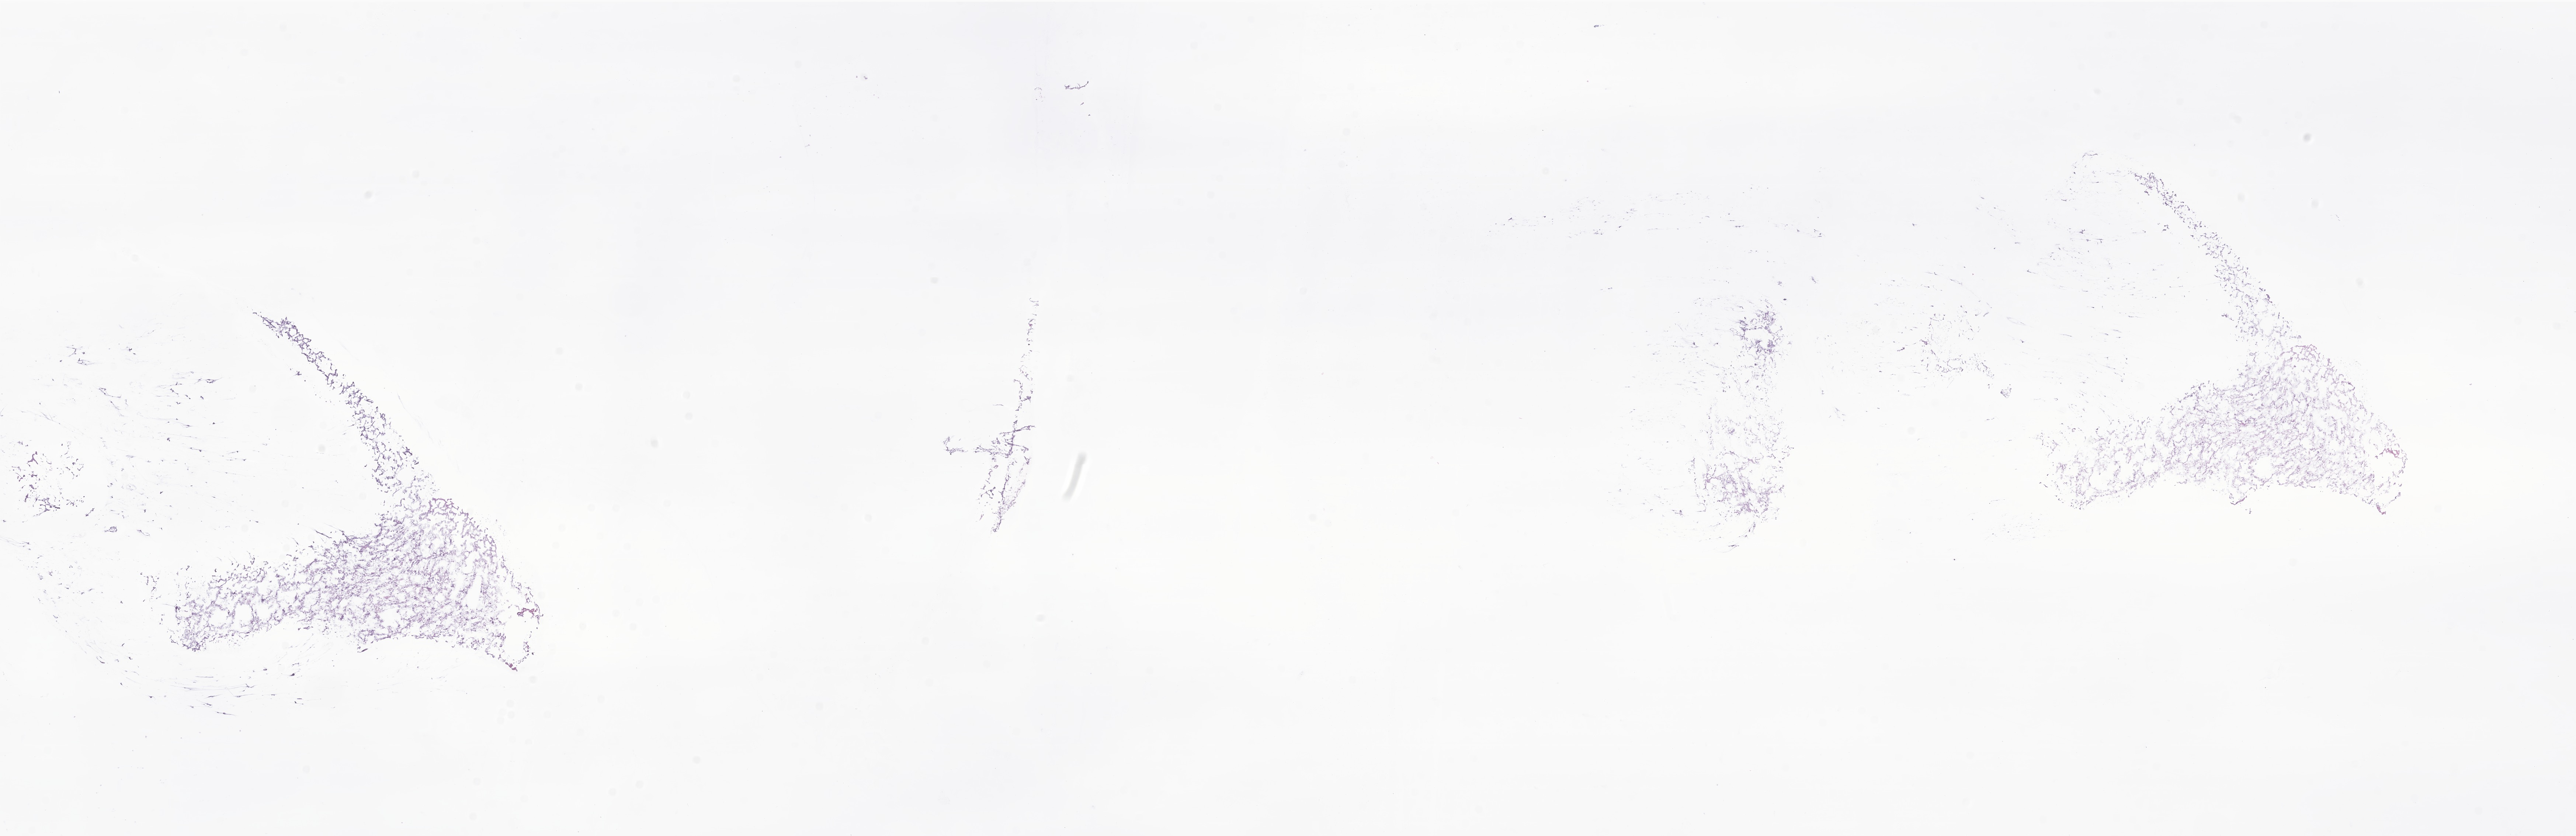
Digitized H&E-stained section of tumor tissue from the brain, a low-resolution overview of the entire scanned area, about 29.5 x 9.6 mm, cryosection (OCT / tissue freezing medium). Female patient, age 109 months (9 years 1 month).
Diagnosis (ICD-O-3 morphology term): Pilocytic astrocytoma.